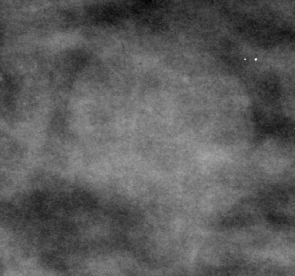
Cropped region of a digitized screen-film mammogram centred on a radiologist-marked abnormality, left breast, CC view, BI-RADS breast density category 2 (scale 1–4).
Finding: mass, shape round / oval, margins circumscribed / obscured; BI-RADS assessment category 4; subtlety rating 5 on a 1 (subtle) to 5 (obvious) scale; pathology (as recorded): benign.